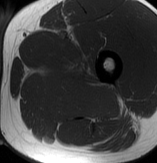
MRI of an extremity soft-tissue mass, one axial slice; position 51 of 70 along the scan axis; MR volume resampled by the dataset authors to the PET/CT grid (not the native acquisition matrix); 3.27 mm slice thickness; 157 × 163 image matrix. Male patient. Case-level facts recorded for this patient, not image findings: histological type: extraskeletal osteosarcoma; grade: high; site of the primary tumour: left adductur.
Structures marked on this image (expert contour drawn on MRI and transferred to this co-registered scan by the dataset authors):
- gross tumour volume (mass): bounding box (x1, y1, x2, y2) in pixels: (33, 56, 121, 120)